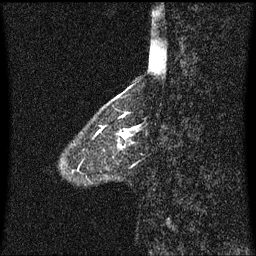
Breast MRI (dynamic contrast-enhanced), one sagittal slice. Position 17 of 60 along the scan axis. Dynamic contrast-enhanced series, image 2 of 3 at this slice position (ordered by acquisition). 1.5 T. TE 4.2 ms, TR 8.4 ms. 256 × 256 image matrix. Patient: female, 58 years.
Structures marked on this image (semi-automatically segmented with operator editing):
- analysis volume of interest (the breast-tissue region the enhancement analysis was run in; not a lesion): bounding box (x1, y1, x2, y2) in pixels: (100, 125, 141, 159)
- tumour enhancement mask (voxels above the 70 % enhancement threshold inside the analysis volume of interest): (100, 127, 137, 147)